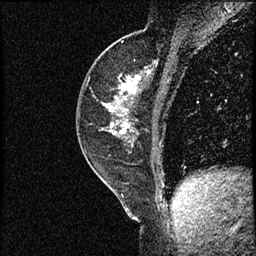
Breast MRI (dynamic contrast-enhanced), one sagittal slice. Position 30 of 56 along the scan axis. Dynamic contrast-enhanced study with each time point stored as its own series, time point 2 of 3 at this slice position (early post-contrast, ordered by acquisition time). 1.5 T. TE 4.2 ms, TR 17.3 ms. 2 mm slice thickness. 256 × 256 image matrix, field of view 200 × 200 mm. Female patient. From the clinical record (not read from this slice): setting: breast cancer imaged before/during neoadjuvant chemotherapy; receptor status: HER2-positive.
Outlined on this slice (semi-automatic segmentation, software-assisted and operator-edited):
- analysis volume of interest (the breast-tissue region the enhancement analysis was run in; not a lesion): box from (x=76, y=50) to (x=156, y=155) px
- tumour enhancement mask (voxels above the 100 % enhancement threshold inside the analysis volume of interest): (x=104, y=72)–(x=150, y=133)